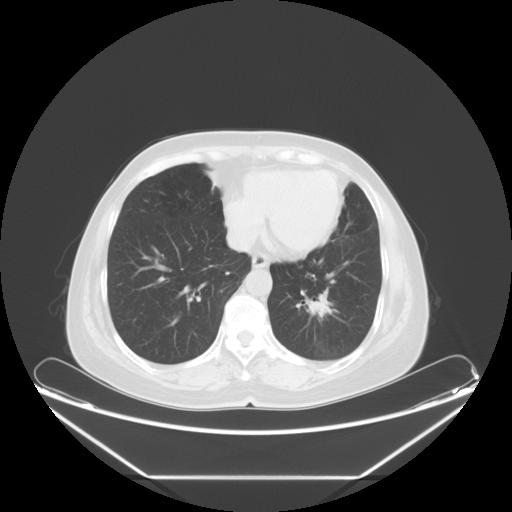
Chest CT, one axial slice; position 21 of 61 along the scan axis; 120 kVp; lung window (W 1500 / L -600 HU); 5 mm slice thickness; 512 × 512 image matrix, field of view 451 × 451 mm. Female patient, age 63 years. From the clinical record (not read from this slice): clinical TNM (as recorded): T1c N0 M0; histopathological grade: G2-3.
Outlined on this slice (bounding box drawn by a radiologist):
- lung tumour (recorded histology: adenocarcinoma): box from (x=307, y=282) to (x=331, y=330) px